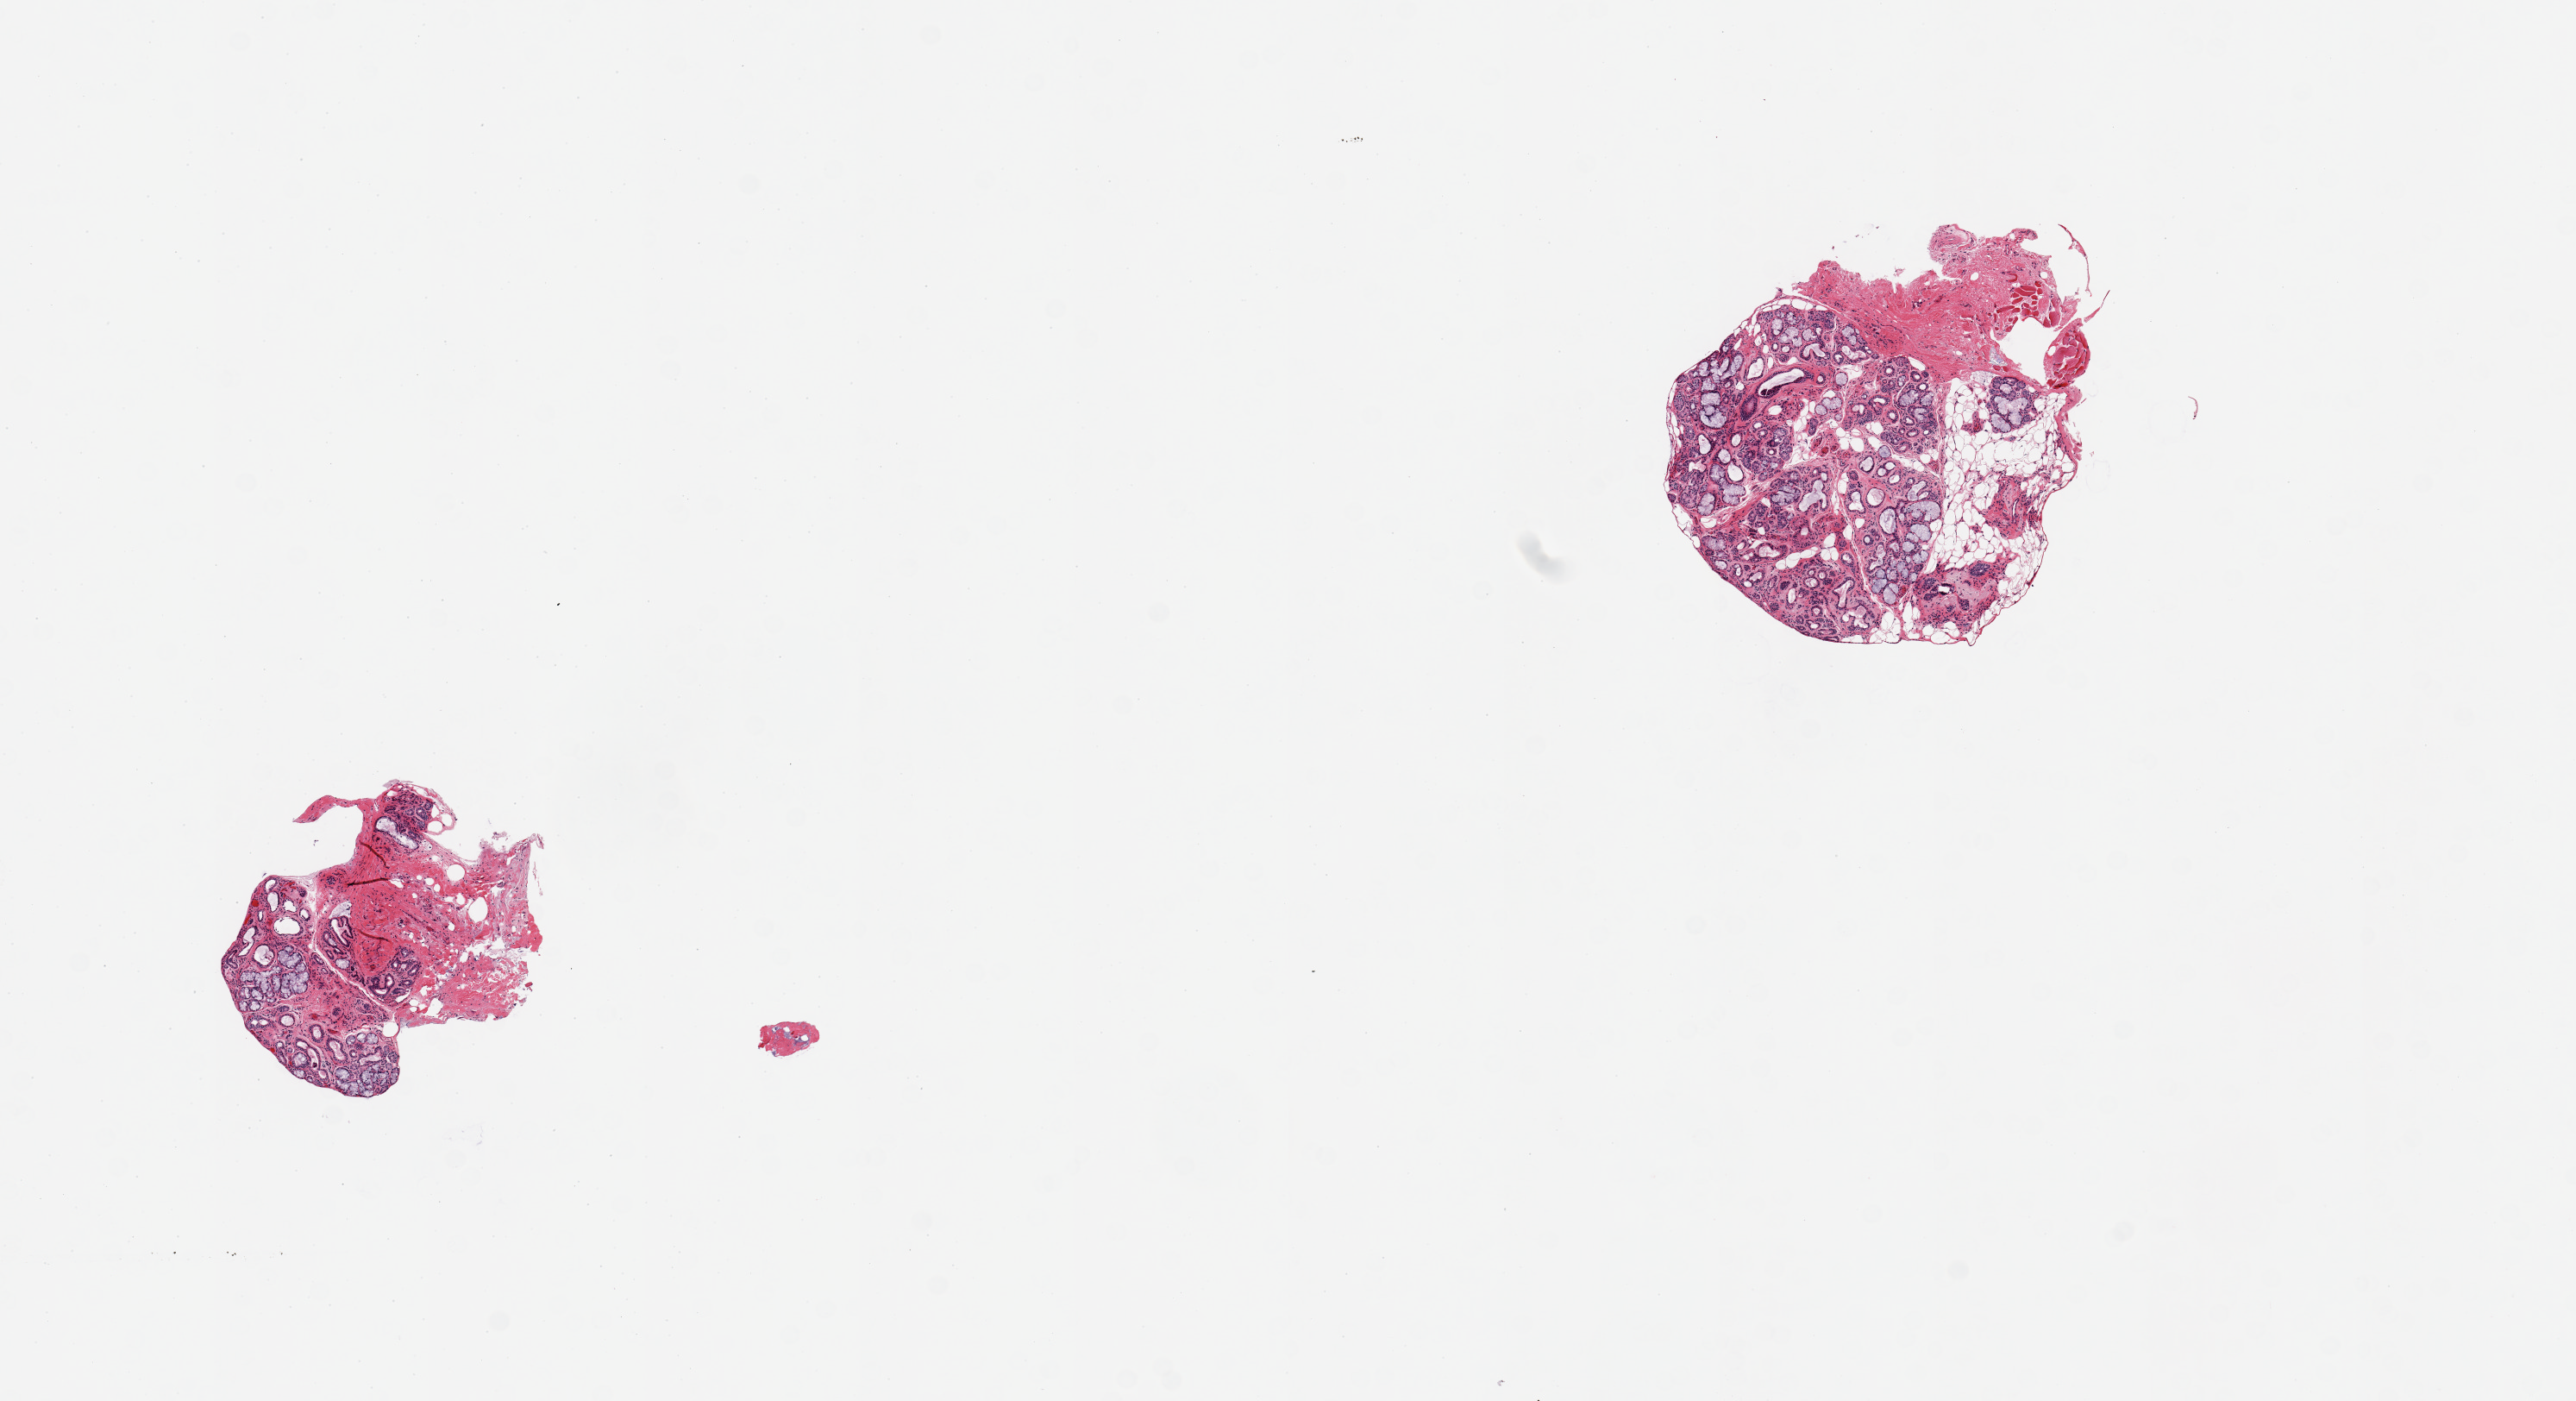
Whole-slide image, hematoxylin and eosin (H&E) stain, brightfield — shown as a low-resolution overview of the whole scanned area (about 11.8 x 6.4 mm), PAXgene-fixed, paraffin-embedded tissue, section of minor salivary gland (target tissue), tissue donor sample. Donor sex: male.
Pathologist's review note for this sample: 2 pieces; salivary gland elements, ~30% fat, stroma, skeletal muscle.